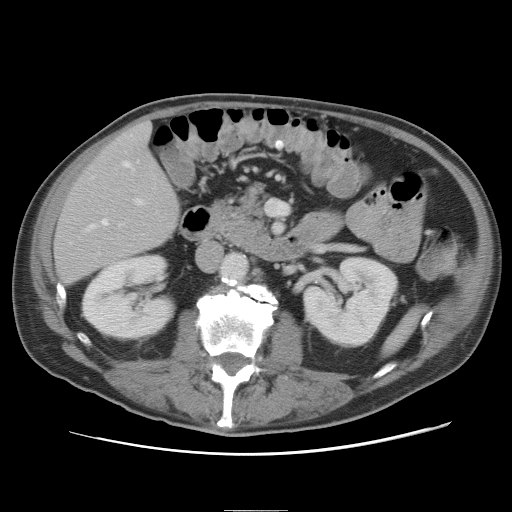
Contrast-enhanced abdominal CT, one axial slice. Intravenous contrast given. Soft-tissue window (W 400 / L 40 HU). 5 mm slice thickness. 512 × 512 image matrix, field of view 375 × 375 mm. Male patient, age 69 years. Case-level facts recorded for this patient, not image findings: diagnosis: colorectal cancer liver metastases, imaged before liver resection; multiple liver metastases: no; largest metastasis: 8.5 cm; chemotherapy before resection: no.
Outlined on this slice (manually delineated by an expert):
- hepatic veins: box from (x=88, y=161) to (x=131, y=230) px
- liver: (x=55, y=122)–(x=179, y=285)
- planned liver remnant (the part of the liver to remain after resection): (x=56, y=122)–(x=179, y=284)
- portal vein (with intrahepatic branches): (x=134, y=198)–(x=144, y=206)